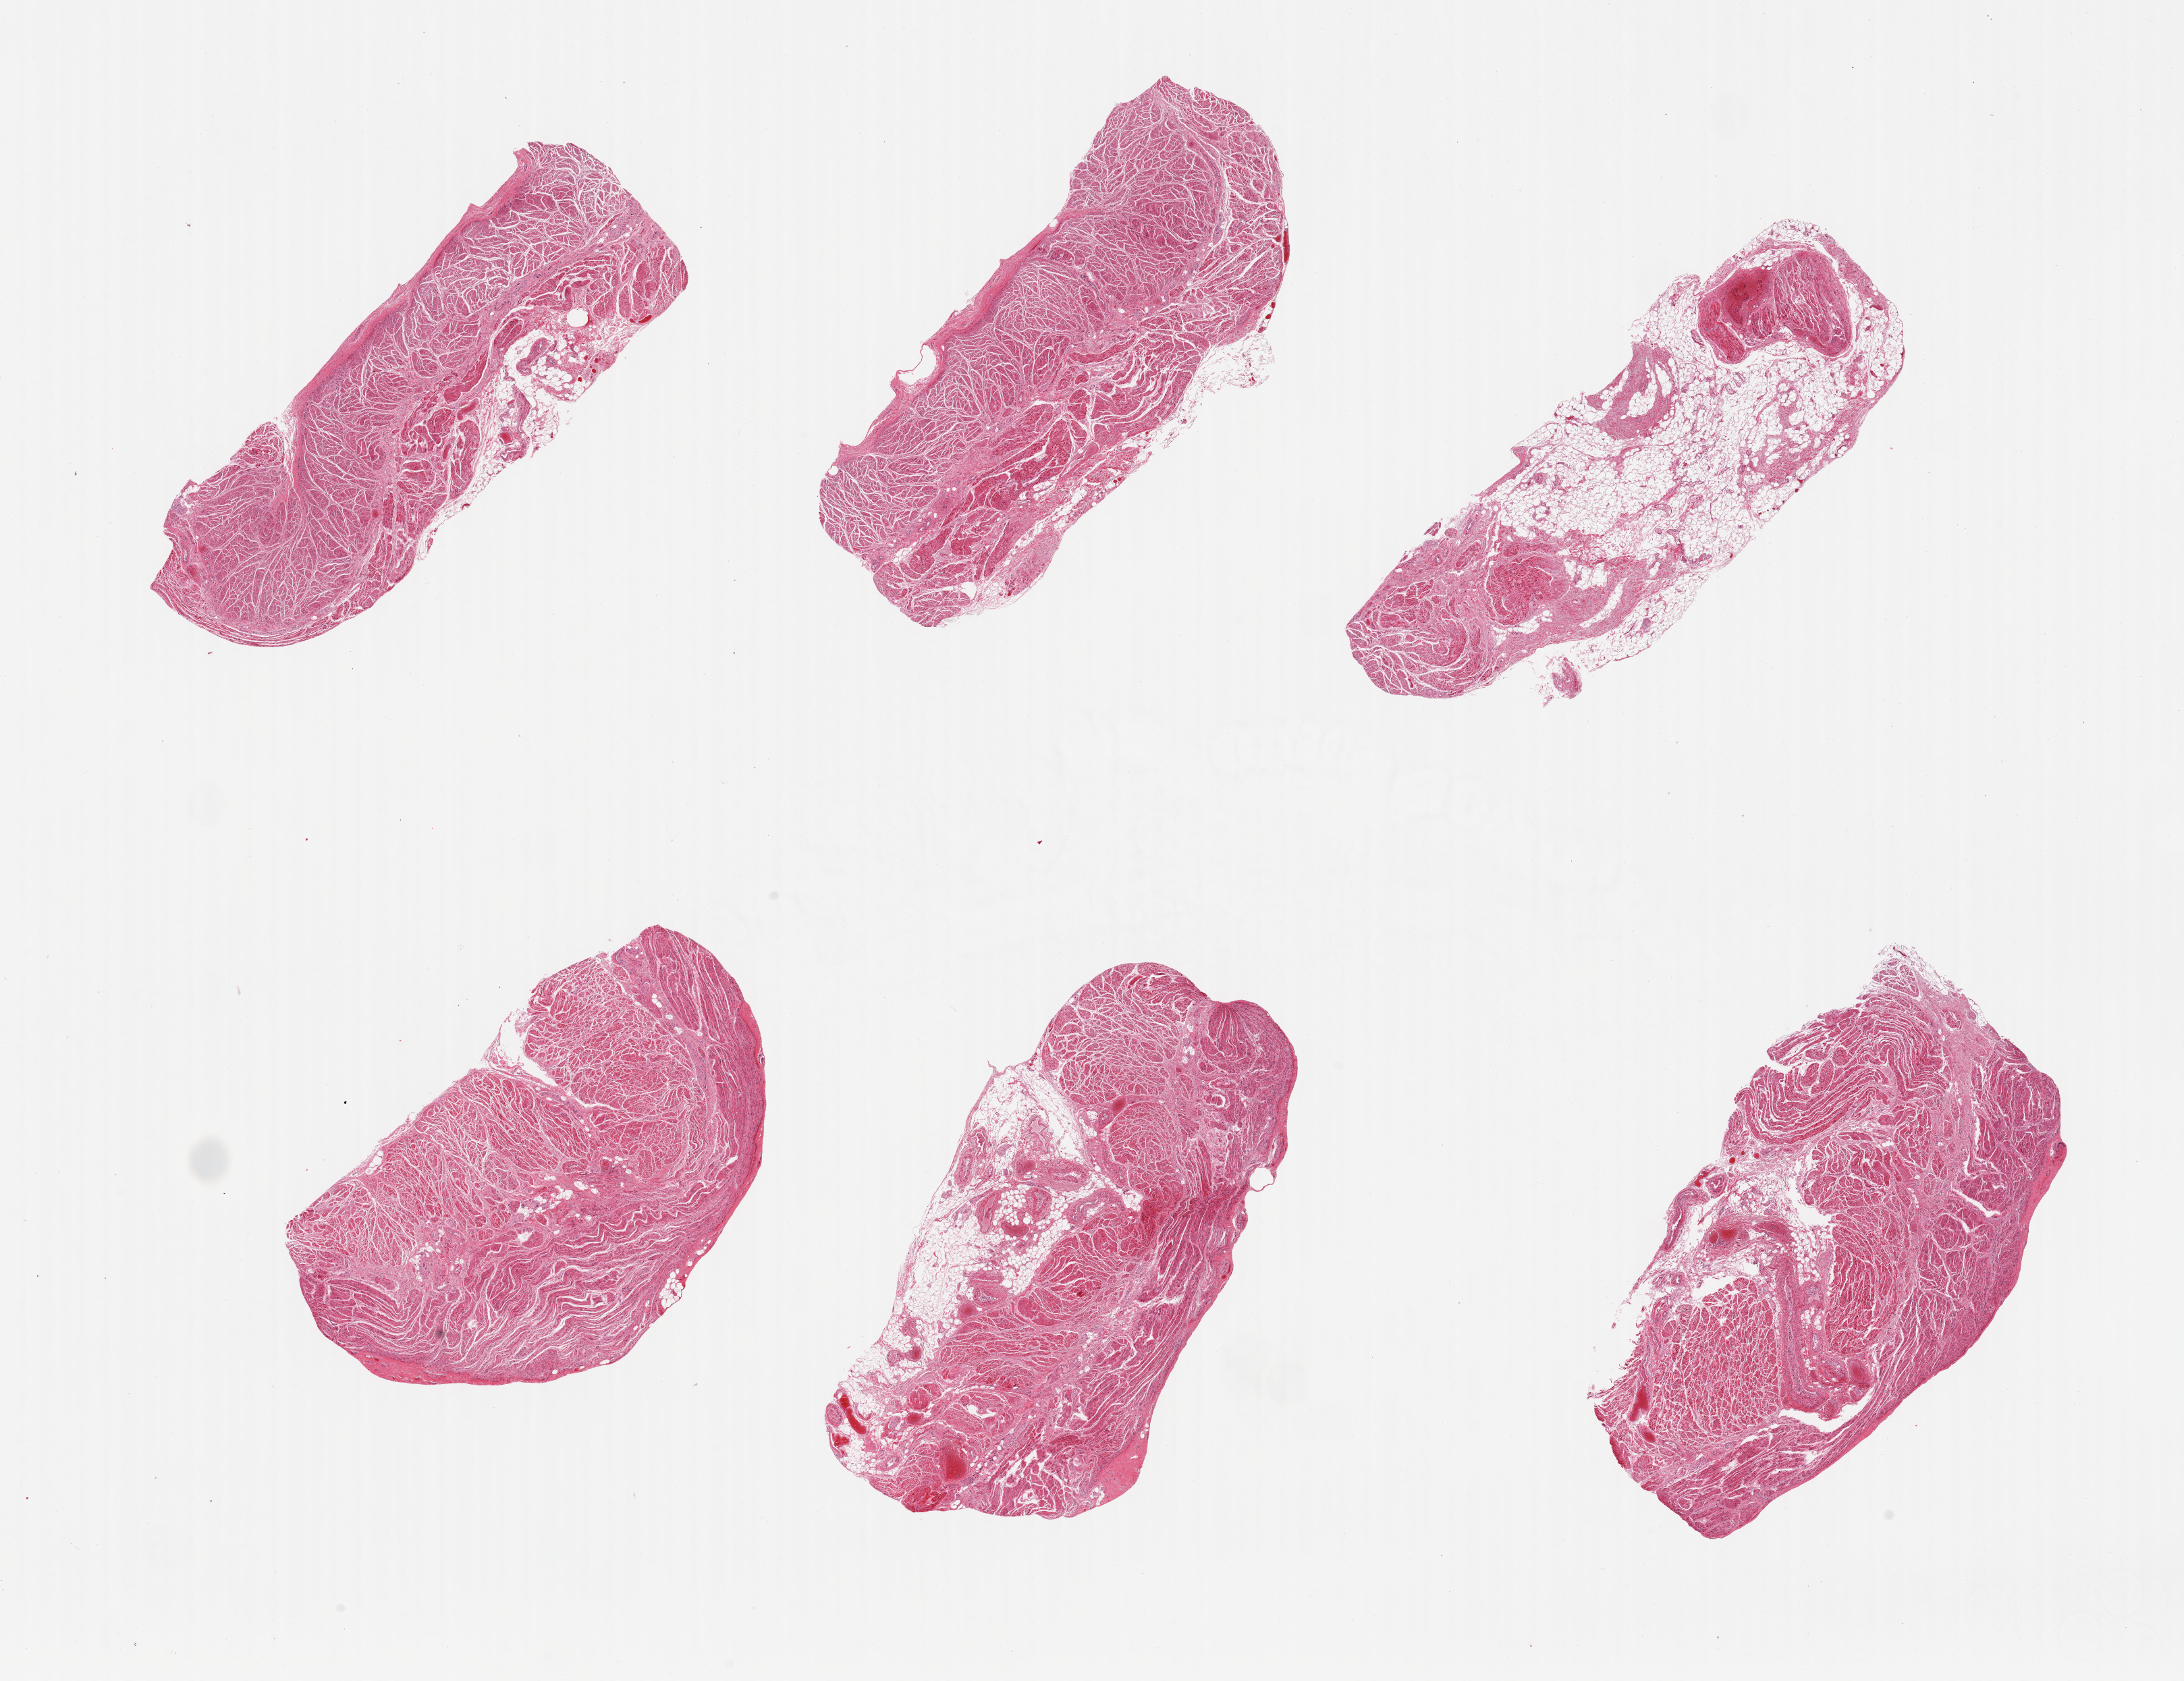
H&E whole-slide image — a low-resolution overview of the entire scanned area, about 25.6 x 19.7 mm. PAXgene-fixed paraffin-embedded (PFPE) section. Target tissue: gastroesophageal junction. Donor tissue sample. Donor sex: male.
Pathologist's review note for this sample: 6 pieces; 1 with 70% fat; 1 with 30% fat.